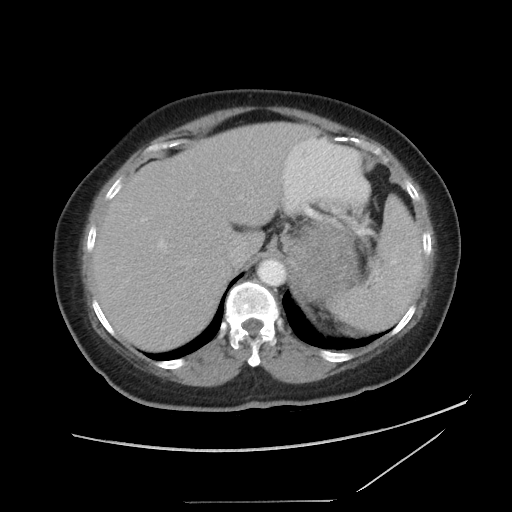
Contrast-enhanced abdominal CT, one axial slice. Slice 66 of 86 in the series (ordered by position). Reconstruction kernel STANDARD. 120 kVp. Intravenous contrast given. Soft-tissue window (W 400 / L 40 HU). 512 × 512 image matrix, field of view 398 × 398 mm. Female patient, age 77 years. From the clinical record (not read from this slice): diagnosis: adrenocortical carcinoma; tumour side: left adrenal; tumour size at pathology: 13.1 cm; Ki-67 index: 10 %.
Structures marked on this image (semi-automatic segmentation, software-assisted and operator-edited):
- mass: box from (x=286, y=227) to (x=357, y=301) px